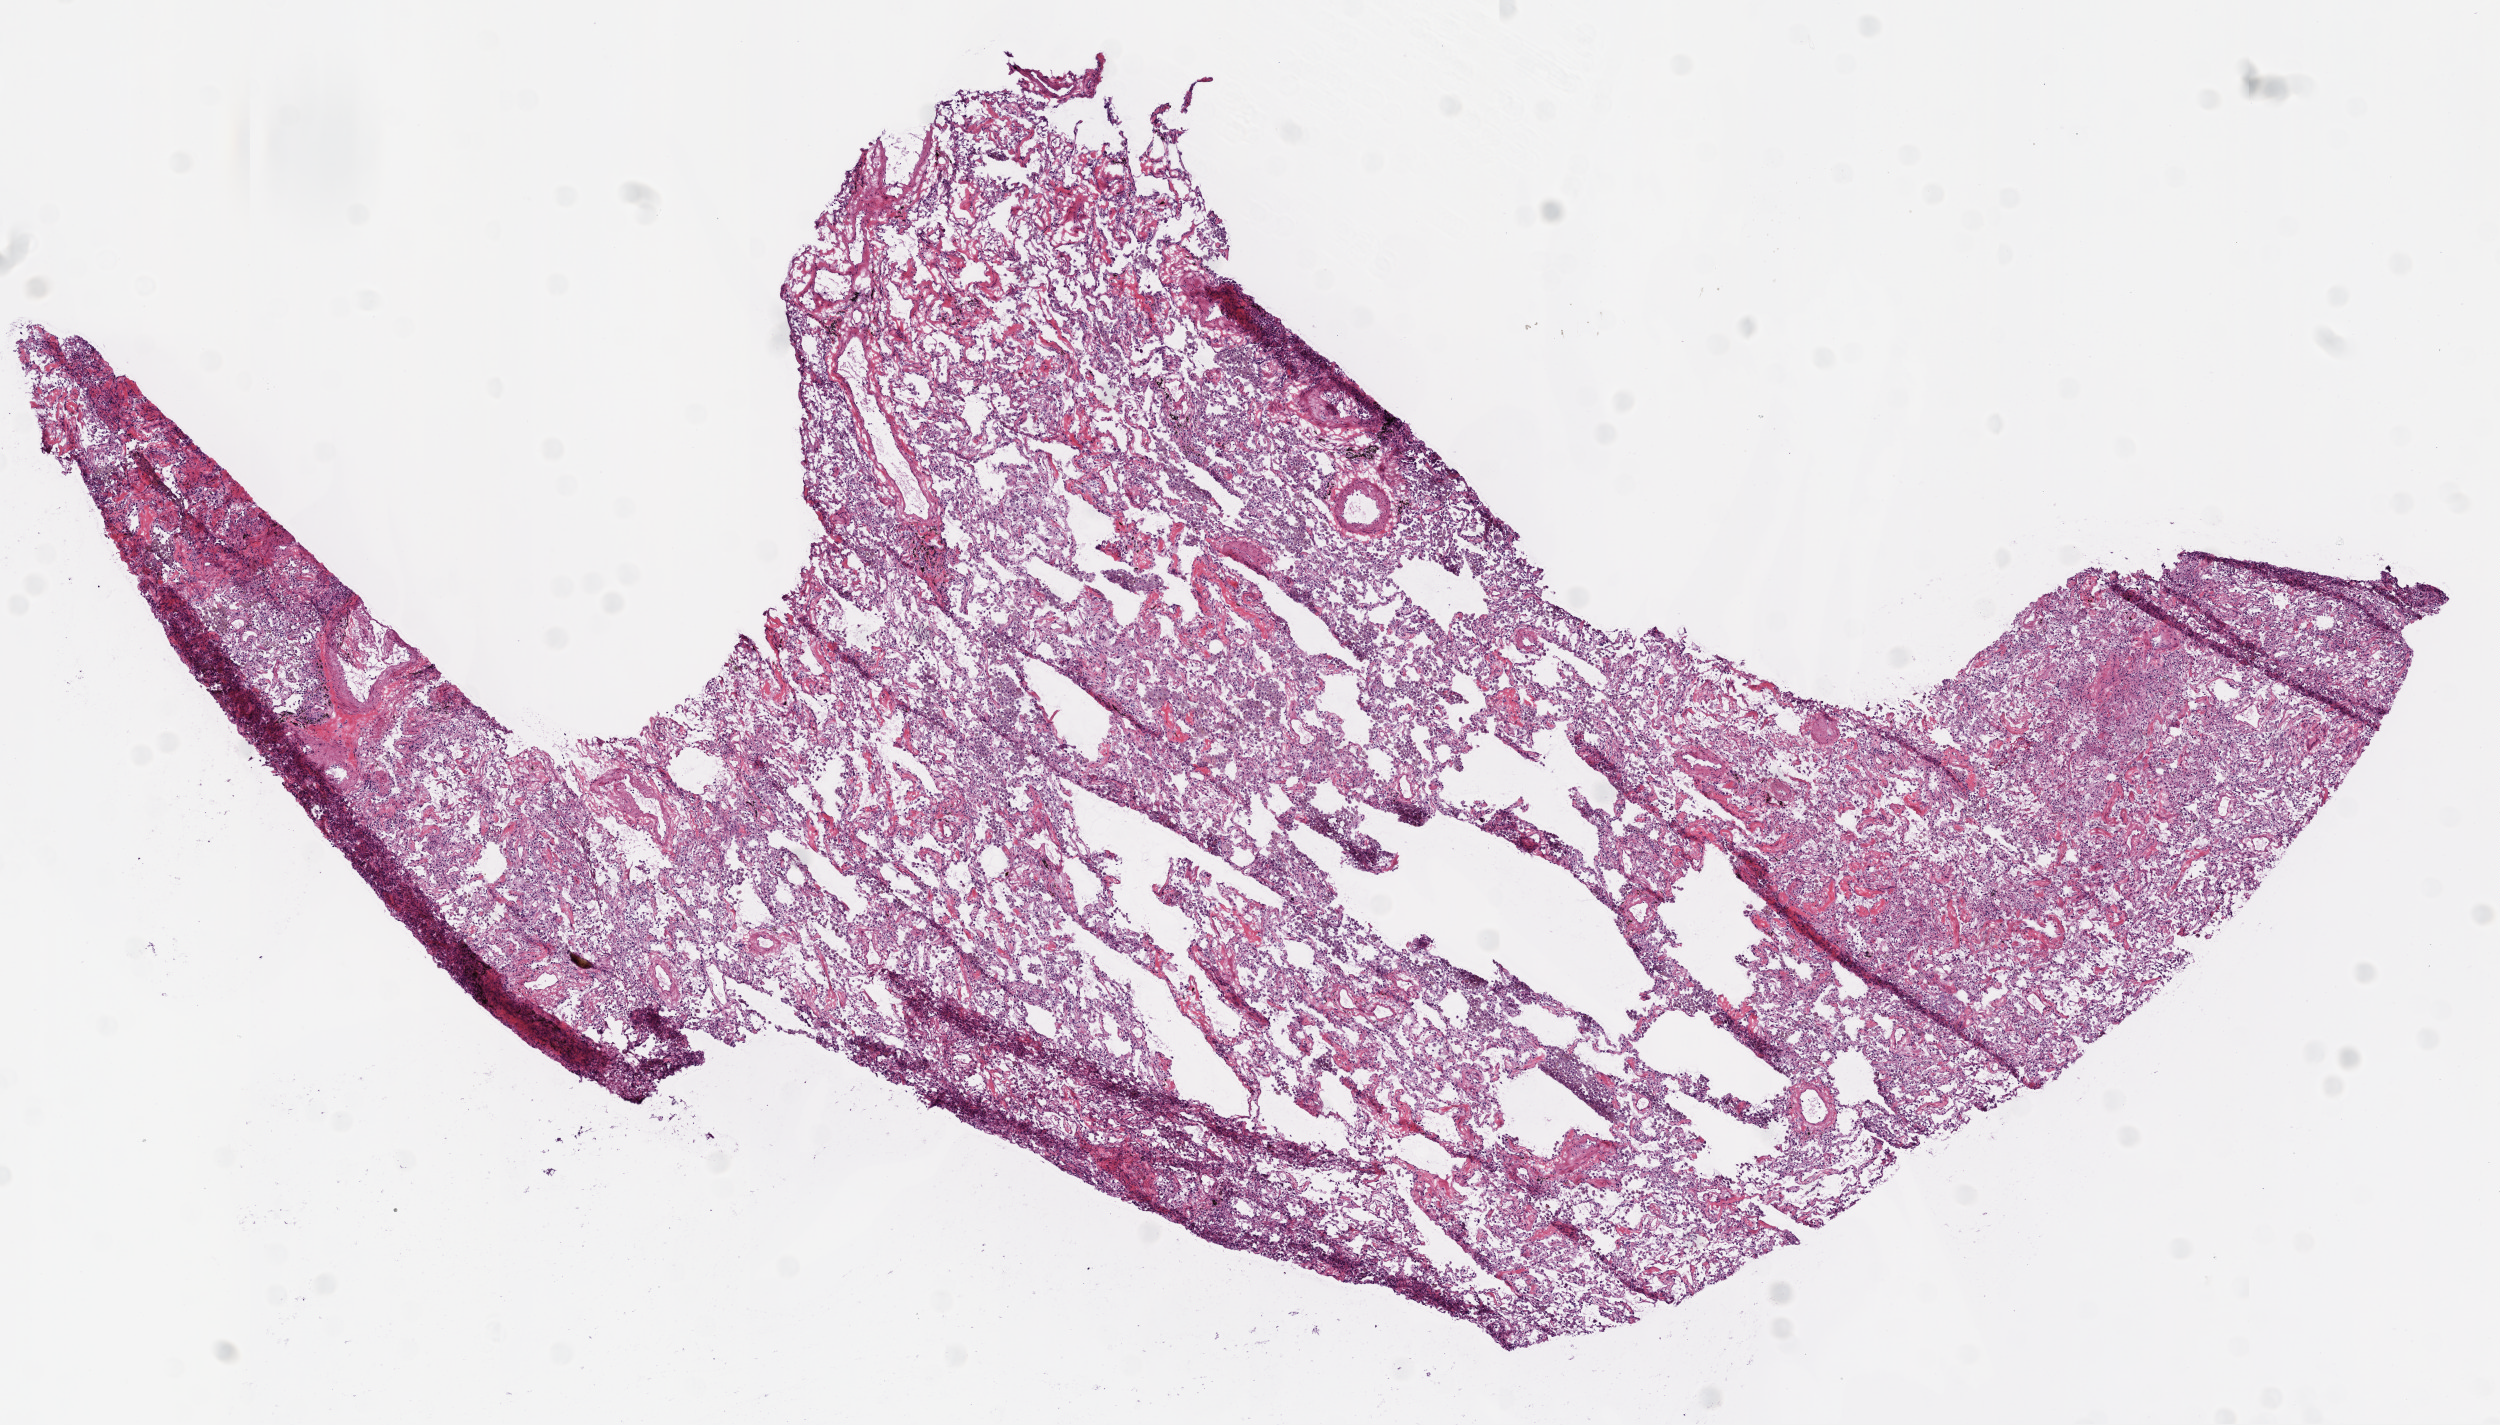
H&E whole-slide image, whole scanned area (about 10.0 x 5.7 mm, acquisition: 20x scan) shown as a low-resolution overview, frozen section, lung, solid tissue normal (non-tumour tissue) sample. Patient: male, age at initial diagnosis 64 years.
• this section: solid tissue normal (non-tumour) sample from the same patient
• patient diagnosis: Squamous cell carcinoma, NOS (lower lobe, lung)